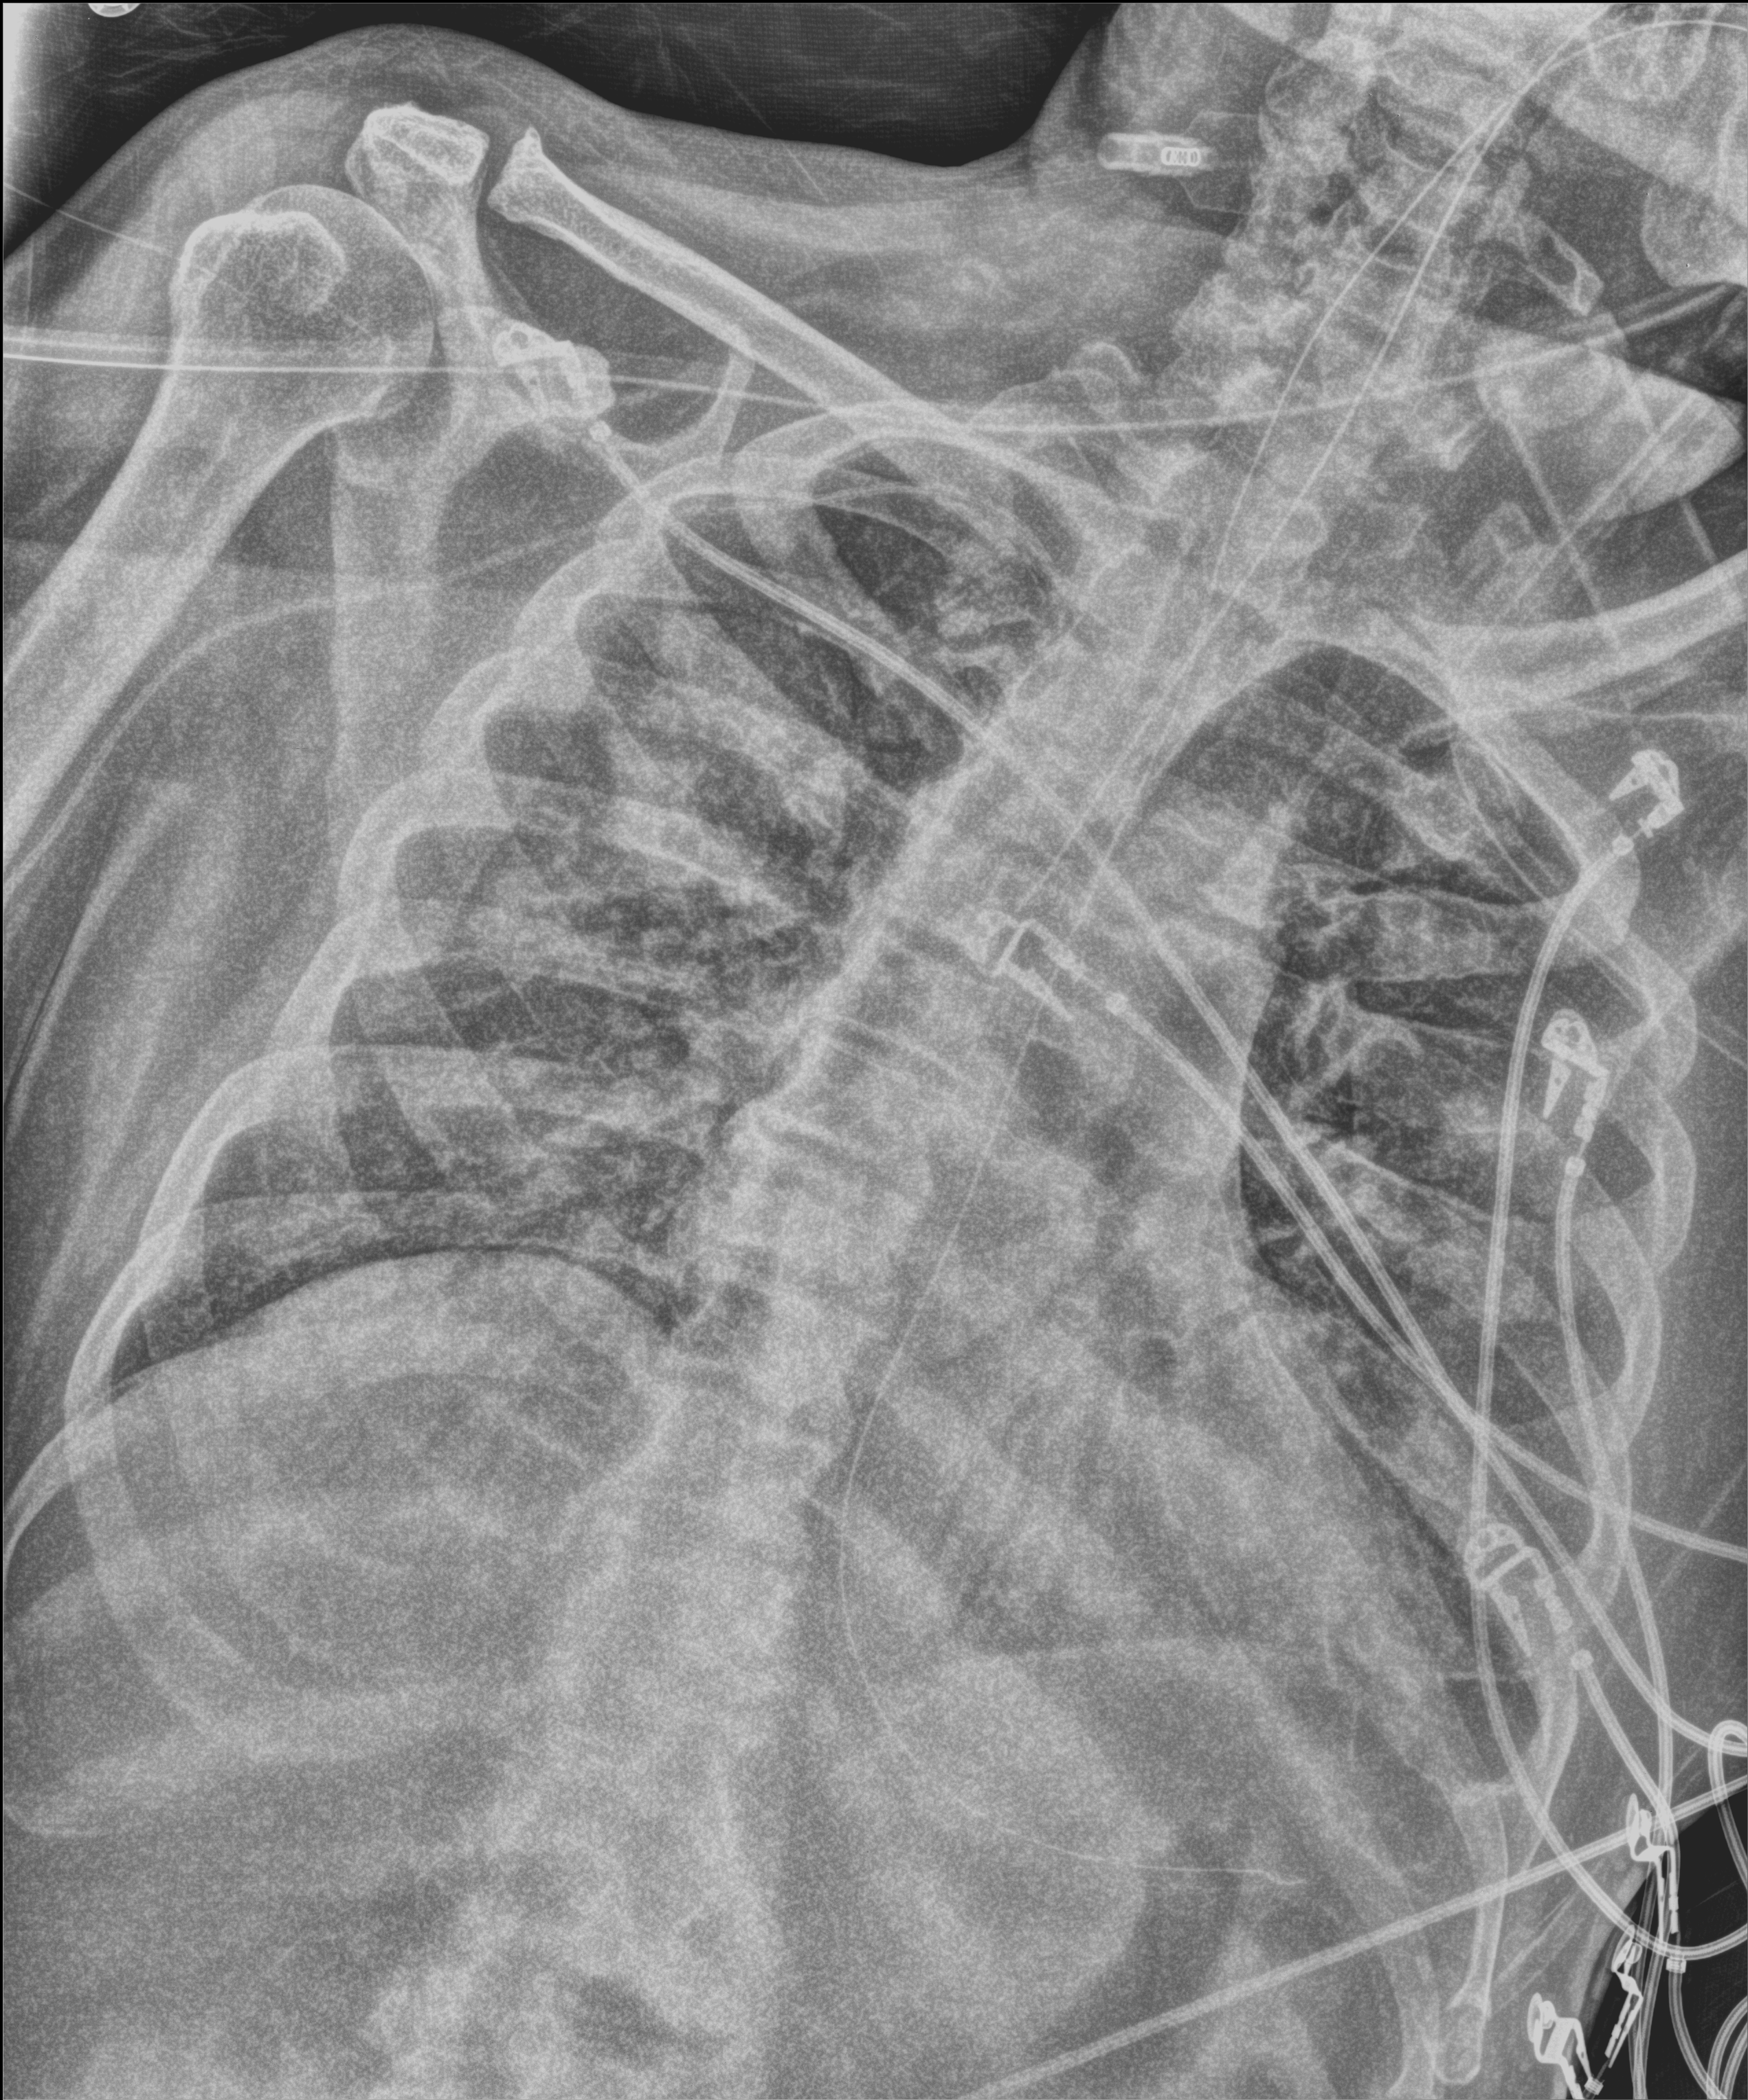
Portable chest radiograph; anteroposterior (AP) projection. Male patient hospitalised with COVID-19, age 75–90 years.
Admission-level facts for this patient (not findings on this image; timing relative to this image not recorded): mechanically ventilated during this hospital stay: yes.